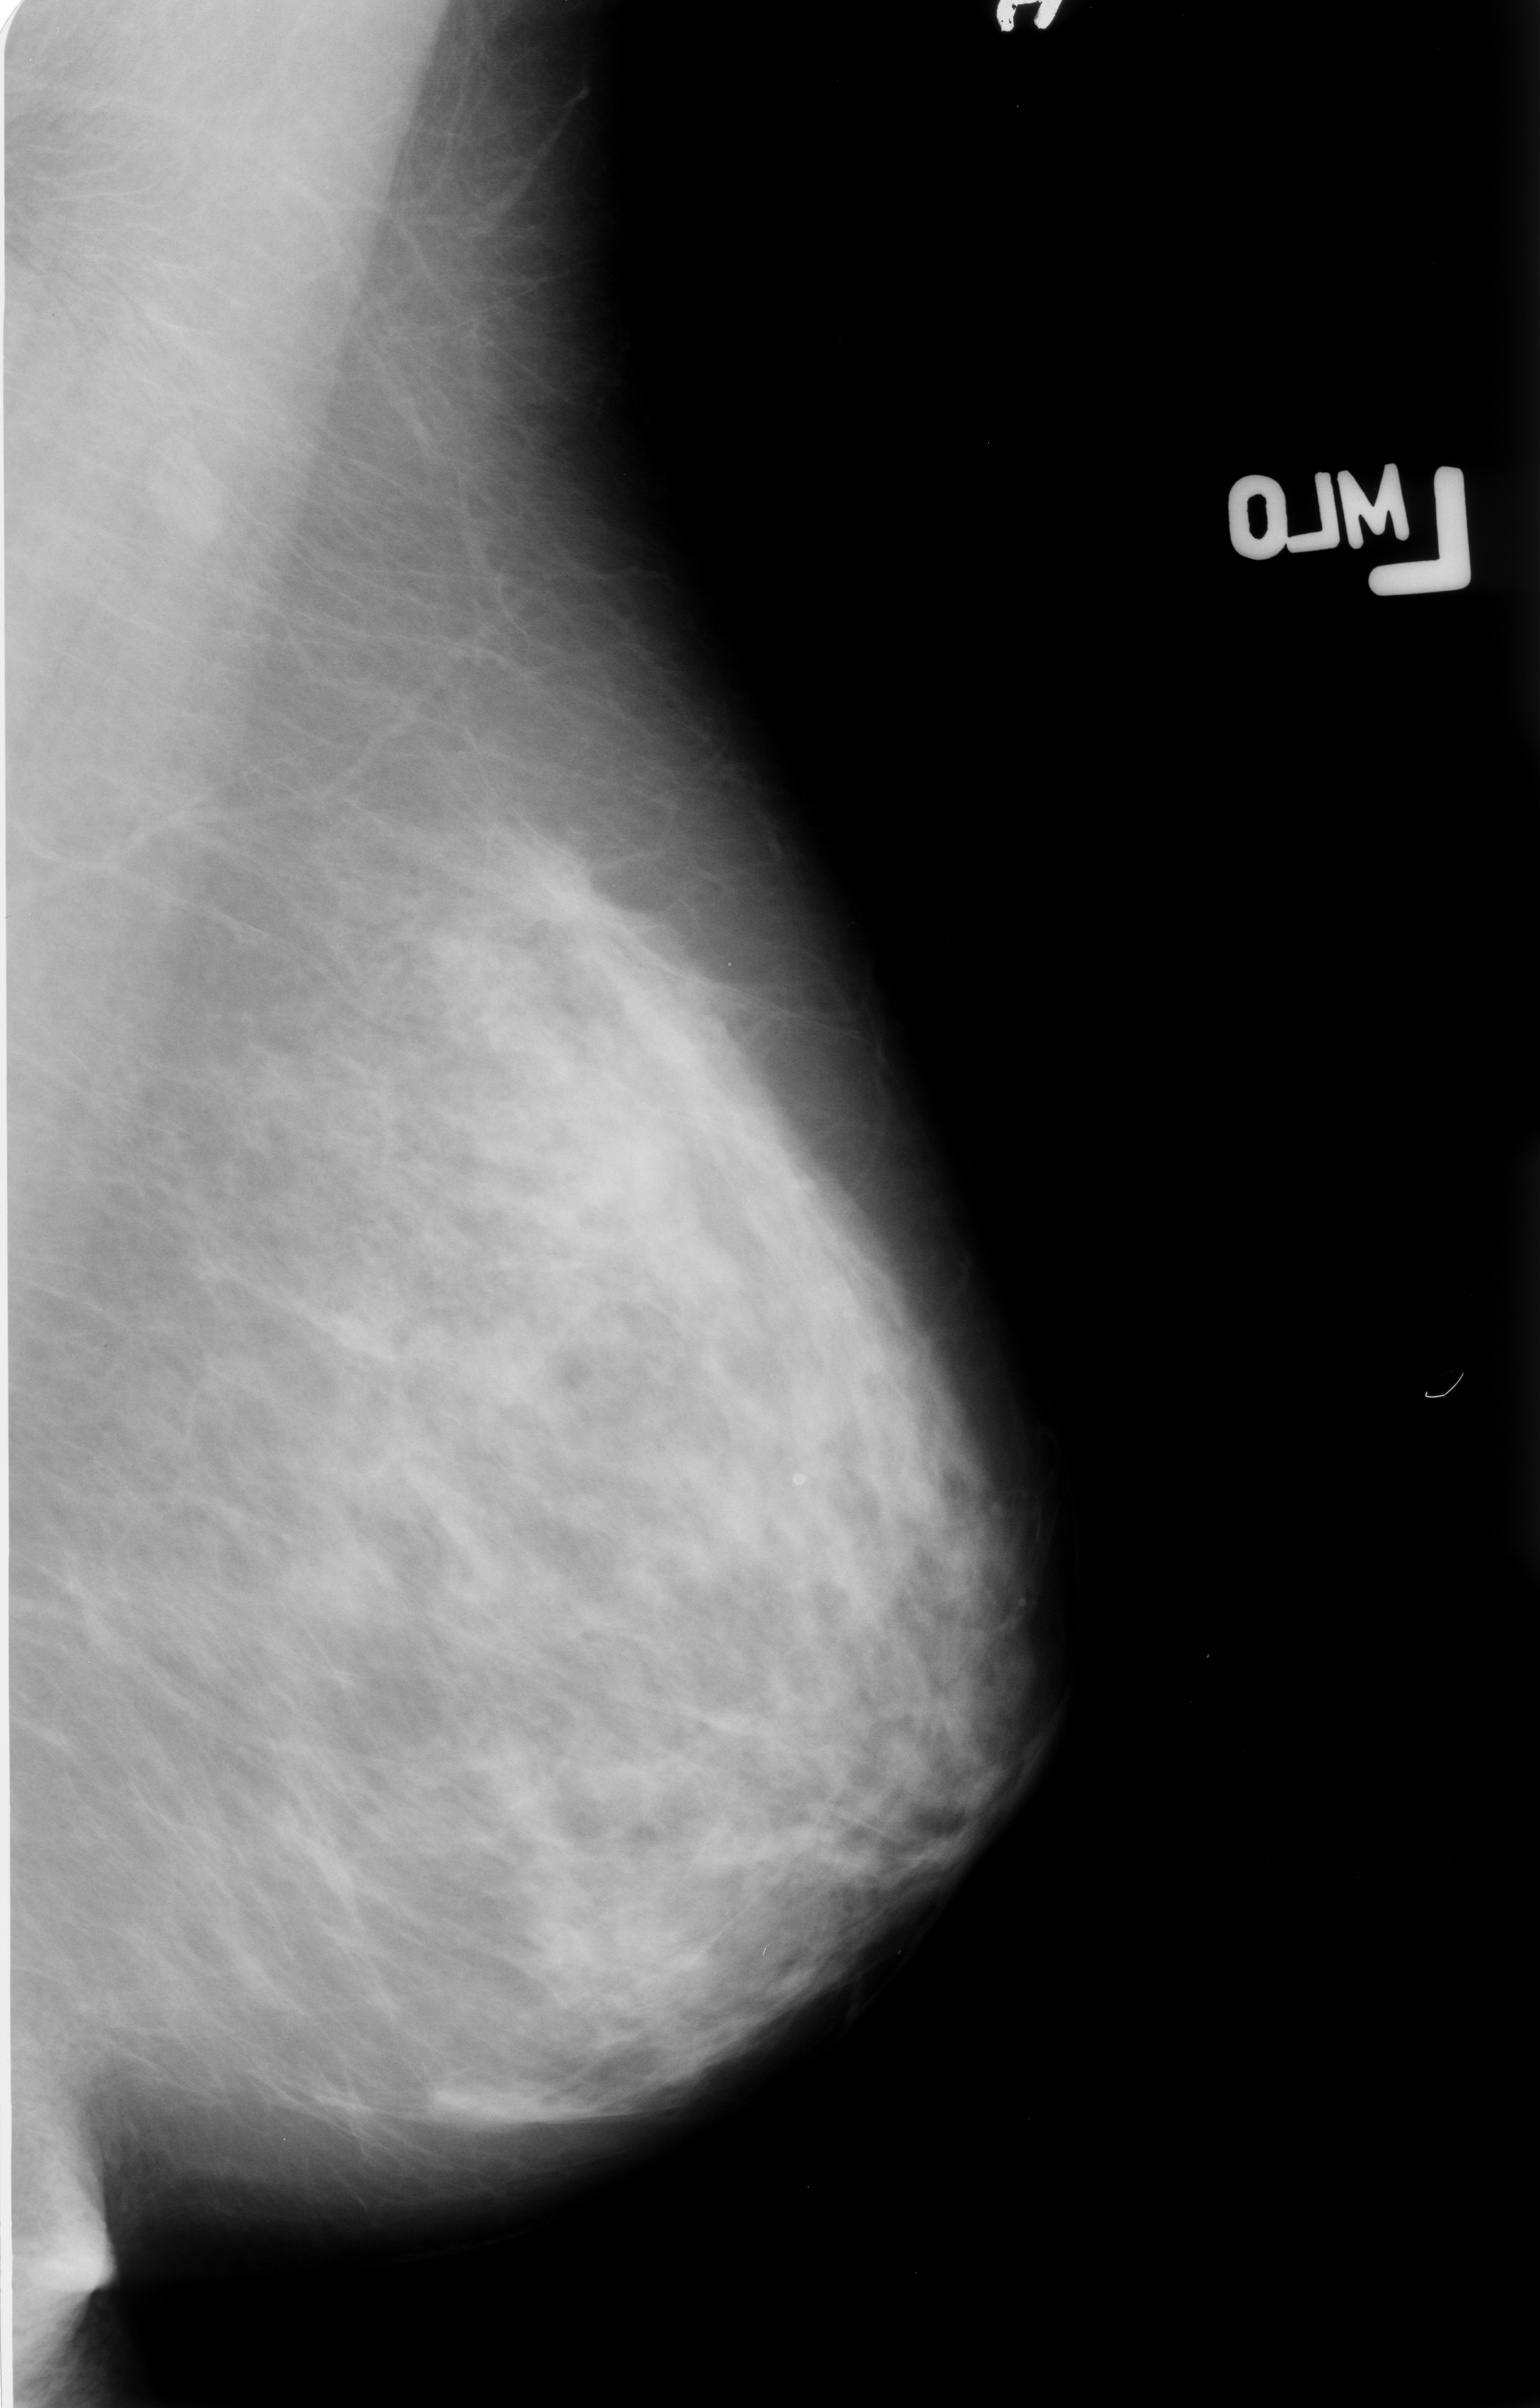
Scanned film-screen mammogram, left breast, MLO view, breast composition: heterogeneously dense (BI-RADS density category 3 of 4).
Mass, shape architectural distortion, margins ill defined / spiculated; BI-RADS assessment category 4; subtlety rating 3 on a 1 (subtle) to 5 (obvious) scale; pathology result (as recorded, not read from the image): malignant.